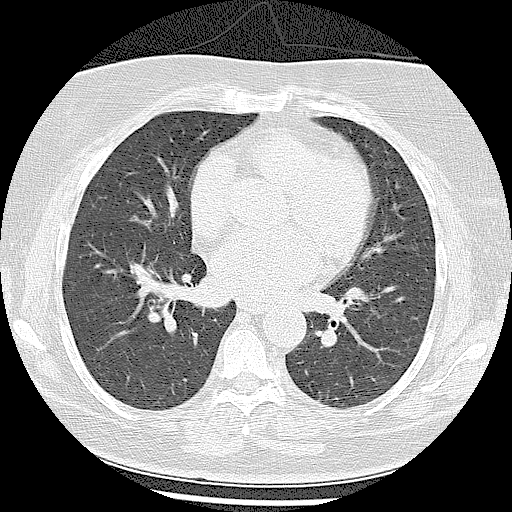
Low-dose screening chest CT, one axial slice. Slice 46 of 102 in the series (ordered by position). Reconstruction kernel LUNG. 120 kVp. Lung window (W 1500 / L -600 HU). 512 × 512 image matrix, field of view 350 × 350 mm.
Outlined on this slice (manually delineated by an expert):
- lesion 1 (tumor, middle lobe of right lung): bounding box (x1, y1, x2, y2) in pixels: (128, 215, 152, 231)